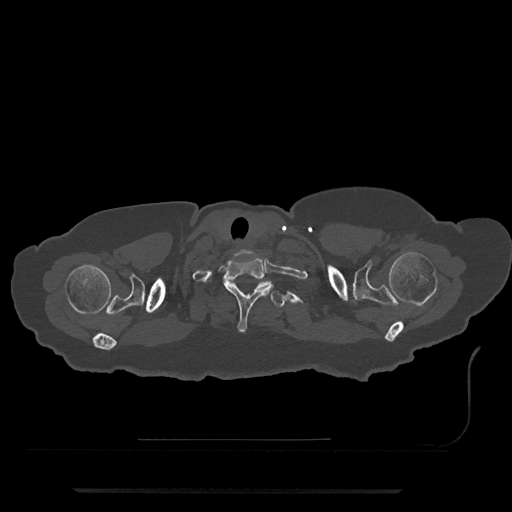
CT including the spine, one axial slice. Position 704 of 797 along the scan axis. 120 kVp. Bone window (W 1800 / L 400 HU). 512 × 512 image matrix. Patient: female, 51 years. Case-level facts recorded for this patient, not image findings: primary cancer: neuro; vertebrae with lytic lesions (as recorded): T8.
Annotated regions visible in this slice (semi-automatic segmentation, software-assisted and operator-edited):
- T1 vertebra: bounding box [x1, y1, x2, y2] px = [210, 257, 293, 333]
- T2 vertebra: [228, 280, 285, 308]